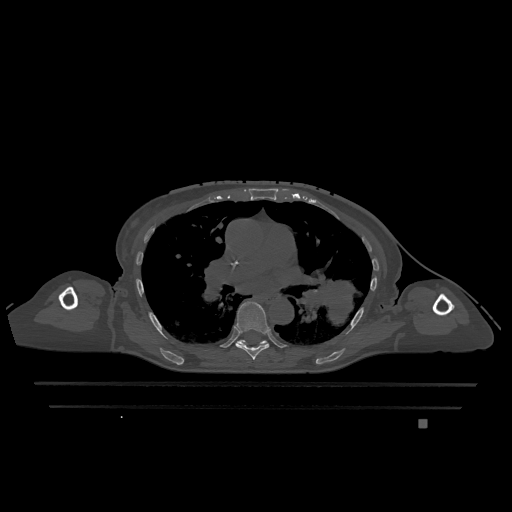
CT including the spine, one axial slice; position 776 of 1317 along the scan axis; bone window (W 1800 / L 400 HU); 0.5 mm slice thickness; 512 × 512 image matrix. Female patient, age 74 years. Case-level facts recorded for this patient, not image findings: primary cancer: lung.
Outlined on this slice (semi-automatic segmentation, software-assisted and operator-edited):
- T6 vertebra: bounding box <235,301,270,360> (left, top, right, bottom; pixels)
- T7 vertebra: <237,340,268,345>